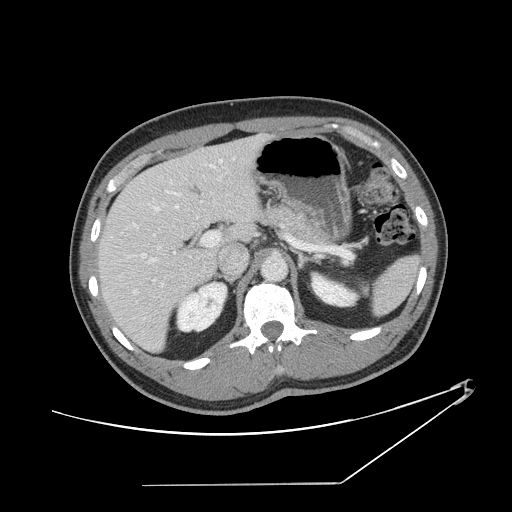
Contrast-enhanced abdominal CT, one axial slice. Position 86 of 152 along the scan axis. 120 kVp. Soft-tissue window (W 400 / L 40 HU). 2.5 mm slice thickness. 512 × 512 image matrix. Male patient, age 45 years. From the clinical record (not read from this slice): diagnosis: colorectal cancer liver metastases, imaged before liver resection; multiple liver metastases: no.
Annotated regions visible in this slice (manually delineated by an expert):
- hepatic veins: bounding box [x1, y1, x2, y2] px = [112, 158, 224, 294]
- liver: [99, 136, 264, 350]
- planned liver remnant (the part of the liver to remain after resection): [99, 156, 224, 350]
- portal vein (with intrahepatic branches): [144, 191, 314, 320]